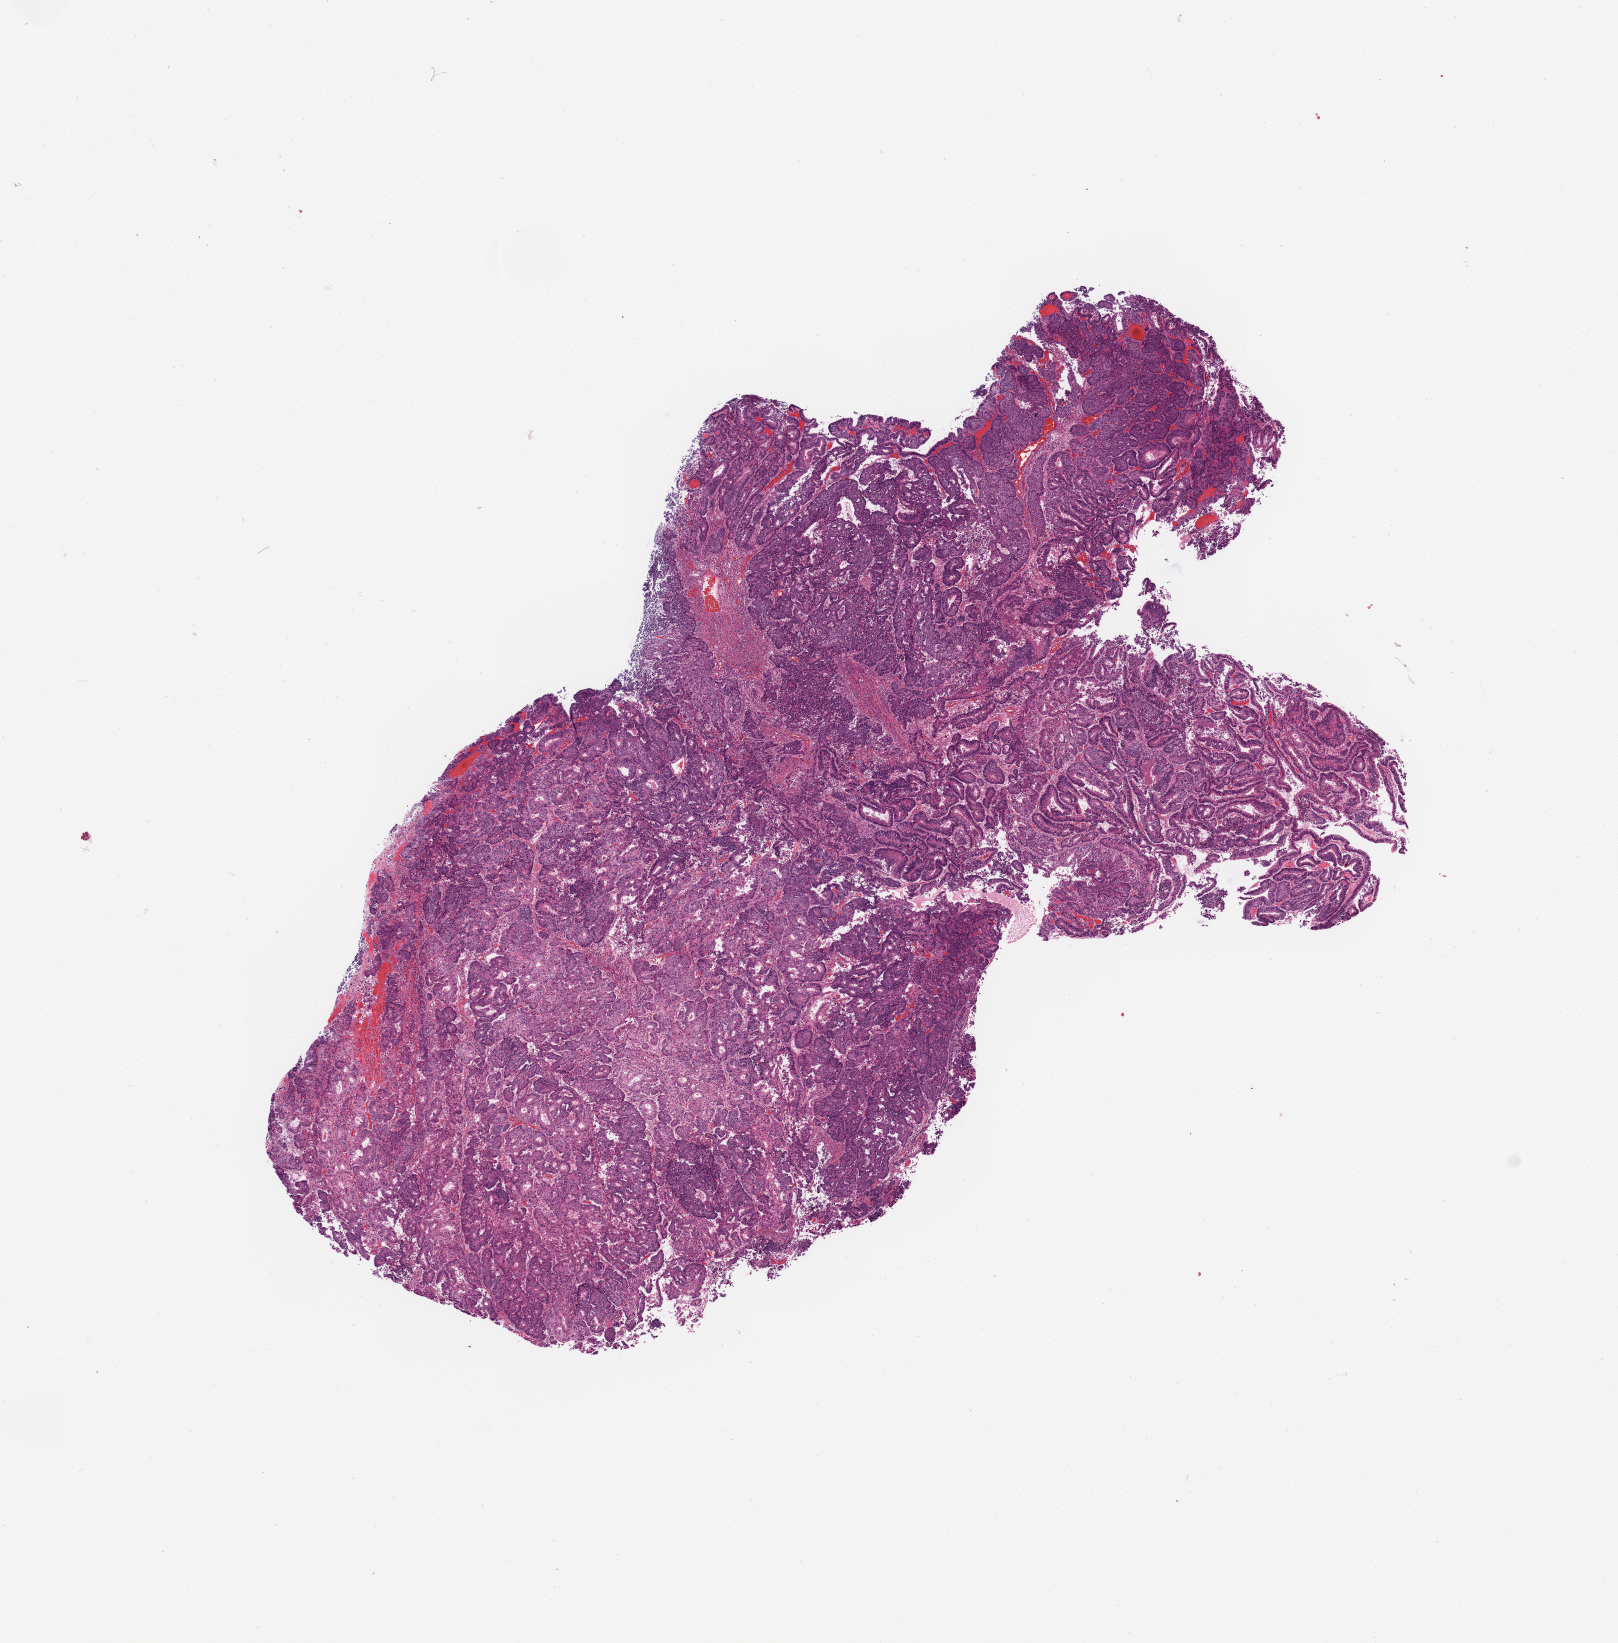
Whole-slide histology image, H&E, a low-resolution overview of the entire scanned area, about 12.8 x 13.0 mm; uterus, tumour tissue. Patient: female, age 50 years. Histologic grade: G1 (well differentiated).
AJCC pathologic stage: III. Diagnosis: Endometrioid adenocarcinoma, NOS.